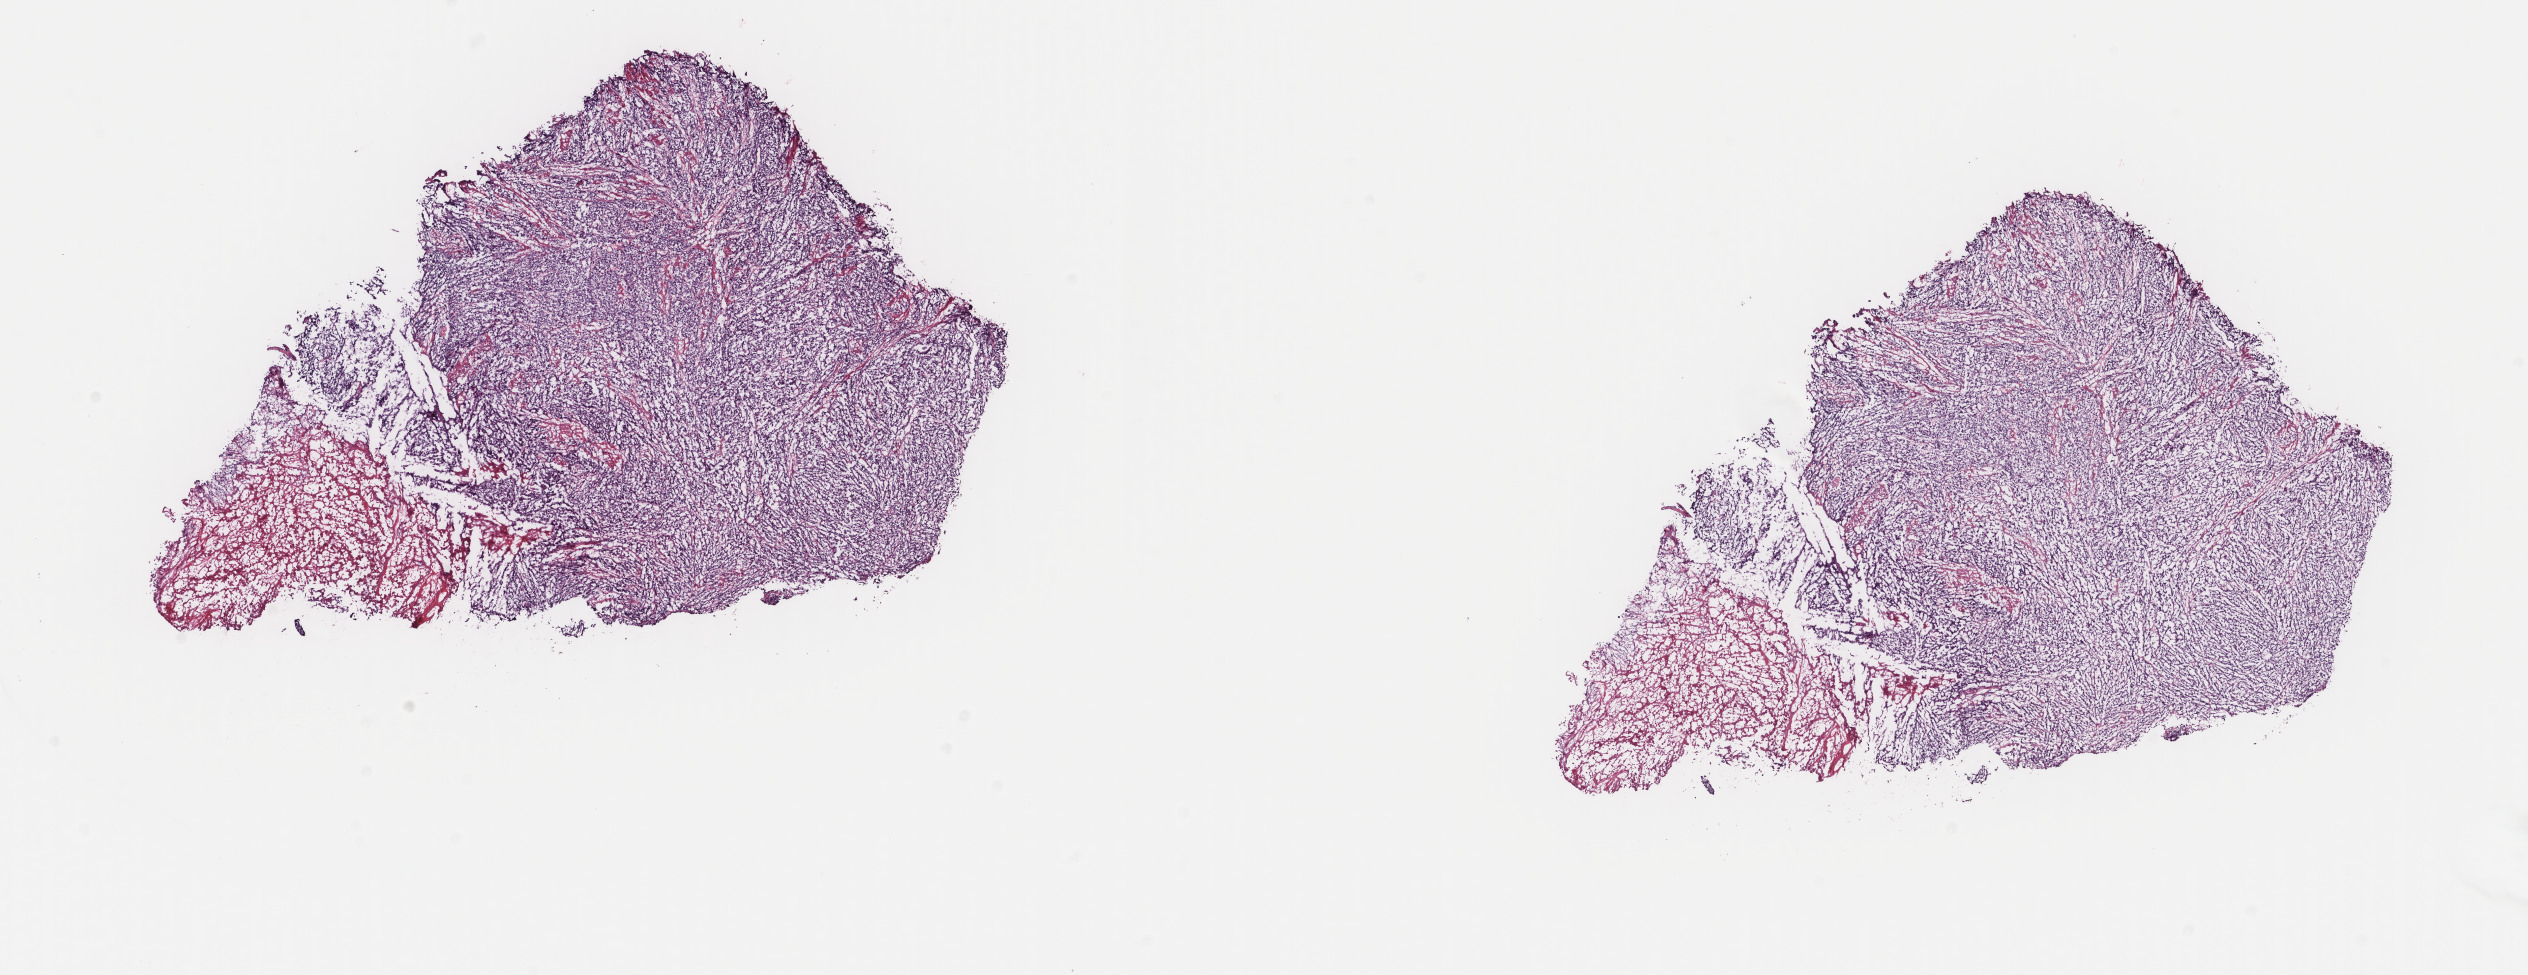
Digitized H&E tissue section (whole slide) — a low-resolution overview of the entire scanned area, about 20.1 x 7.7 mm; frozen section; primary tumour sample from the uterus. Patient: female, age at initial diagnosis 56 years. Histologic grade: G3 (poorly differentiated). Composition of this section per pathologist review: tumour cells 83%, tumour nuclei 98%, normal cells 0%, stromal cells 2%, necrosis 15%. Infiltration values recorded for this section: lymphocyte infiltration 15%, monocyte infiltration 5%, neutrophil infiltration 3%.
Pathologic diagnosis: Endometrioid adenocarcinoma, NOS (endometrium). Lymph nodes positive (case pathology): 1 of 2 examined. FIGO stage: IVB.